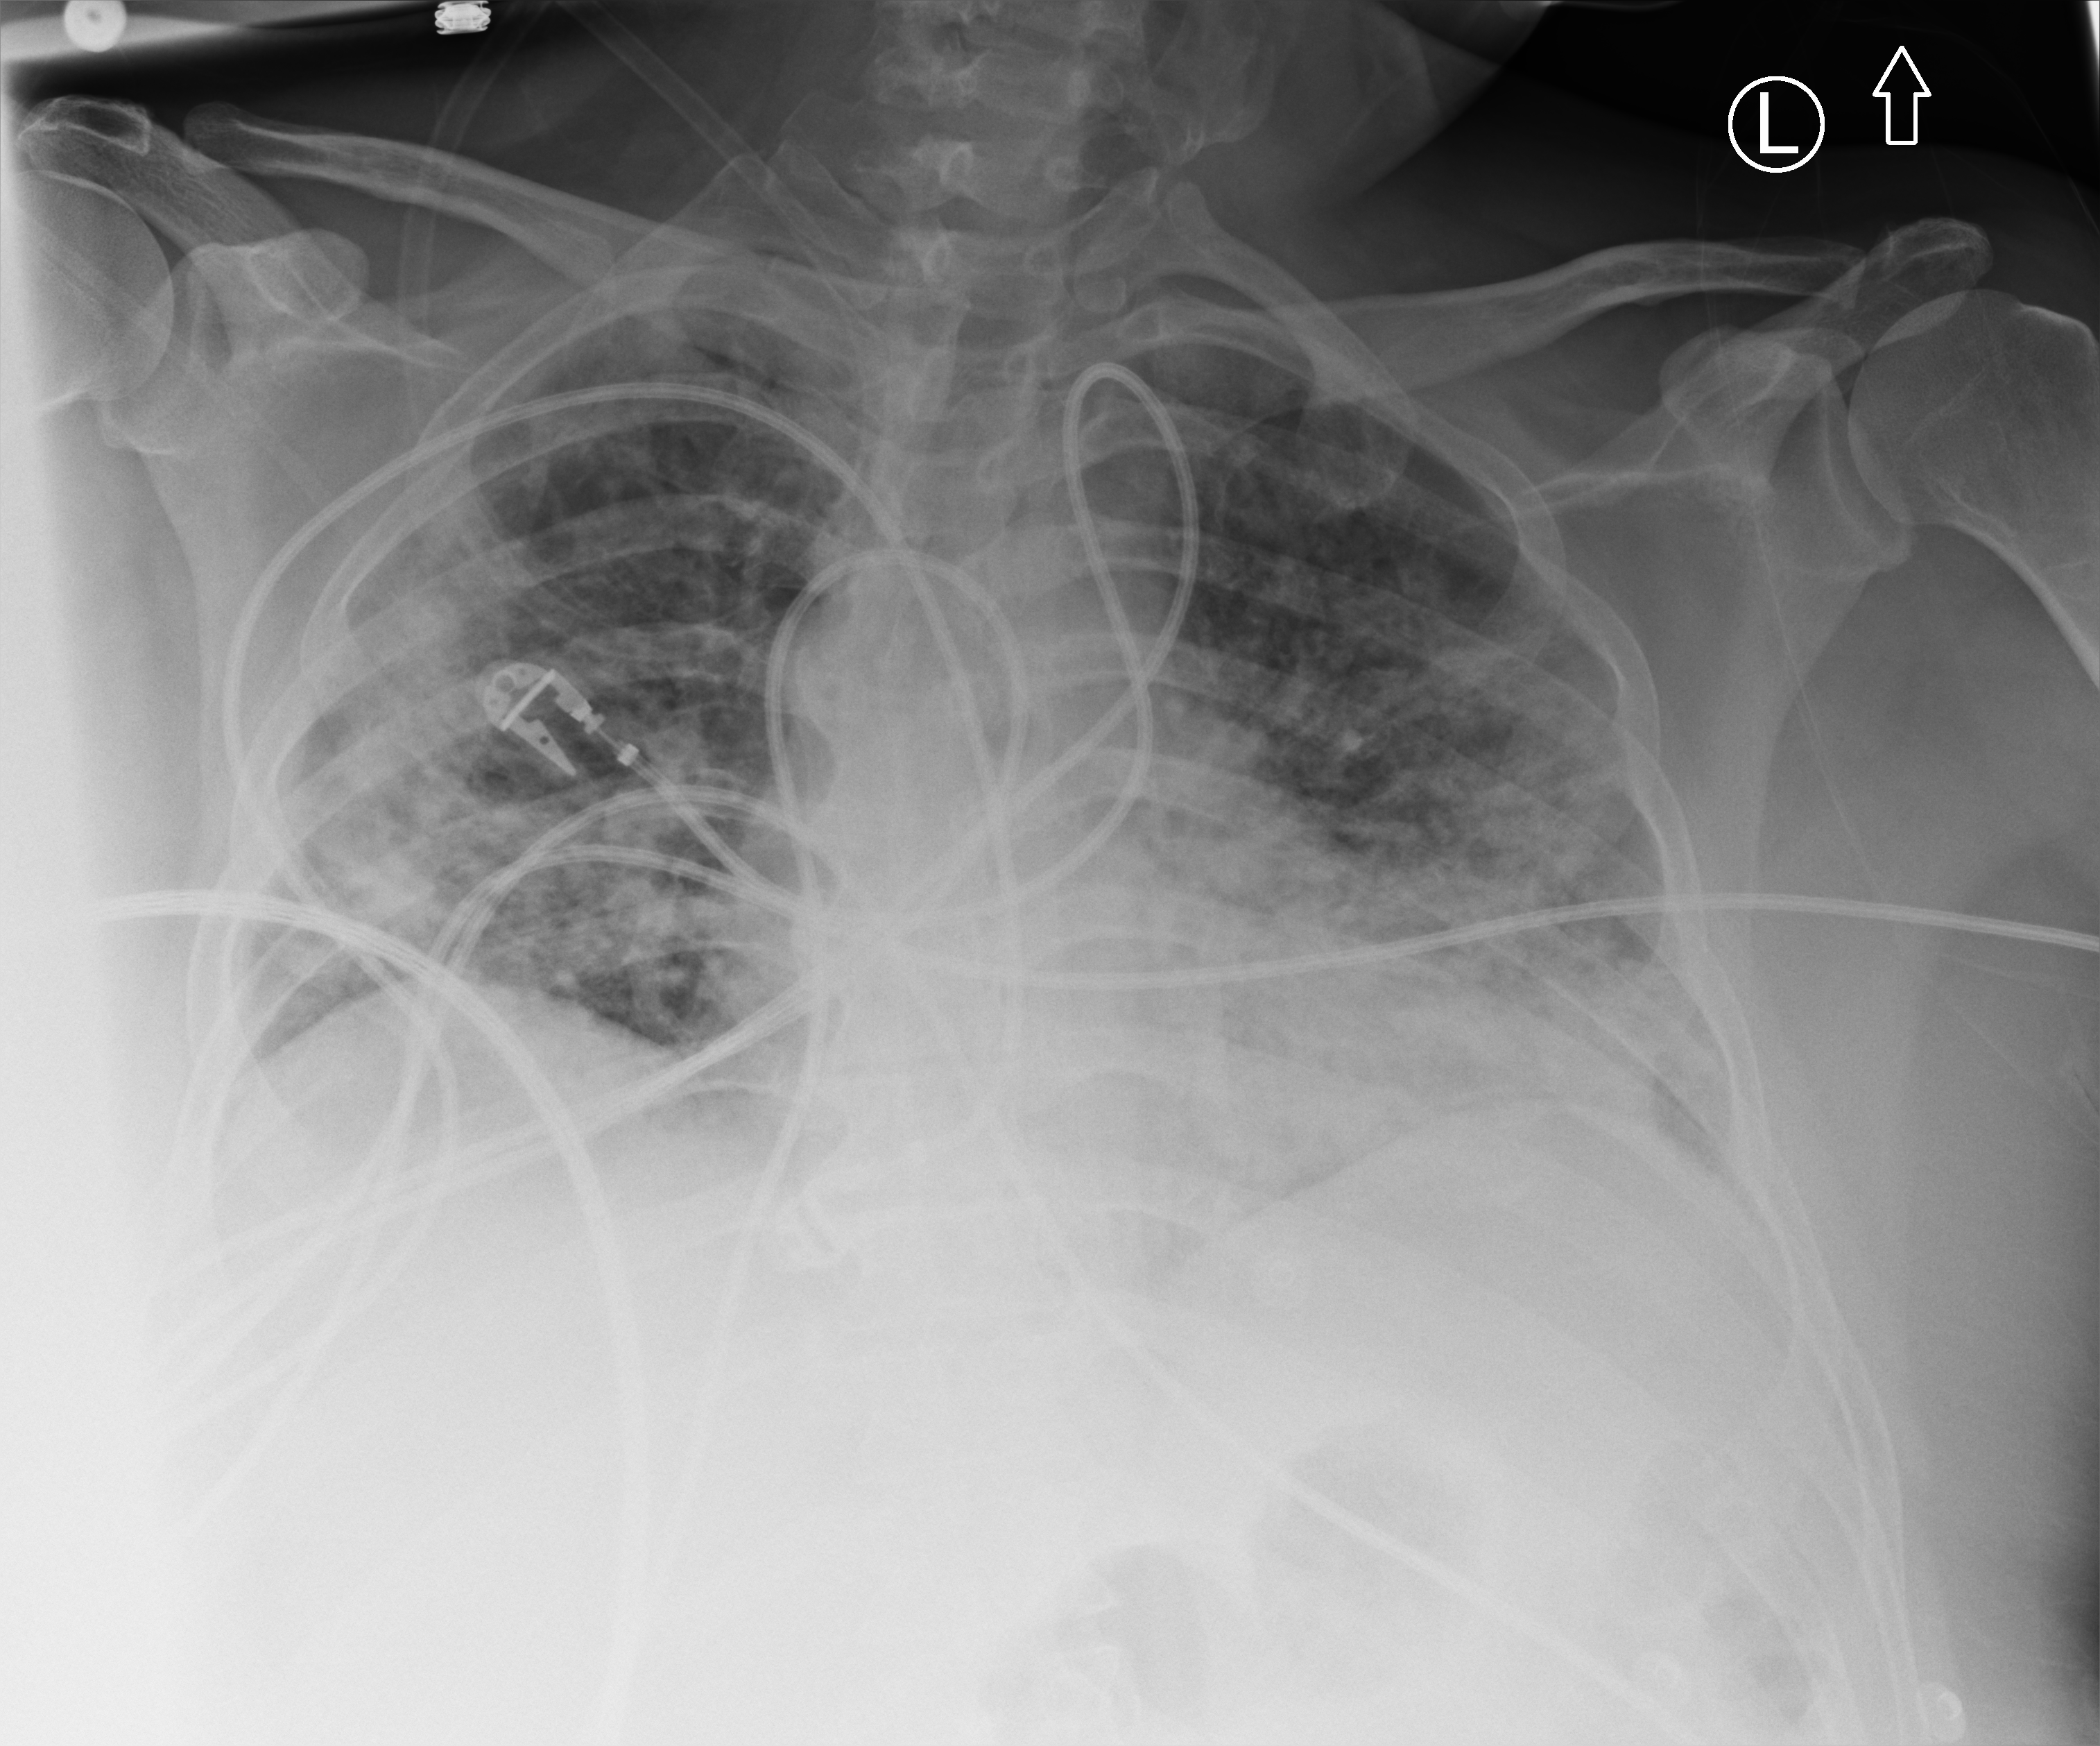
Bedside chest radiograph (computed radiography), anteroposterior (AP) projection. Male patient hospitalised with COVID-19, age 18–59 years.
Hospital-stay facts (about this admission, not read from this image; timing relative to this image not recorded):
- admitted to intensive care during this hospital stay: yes
- length of hospital stay: 24 days